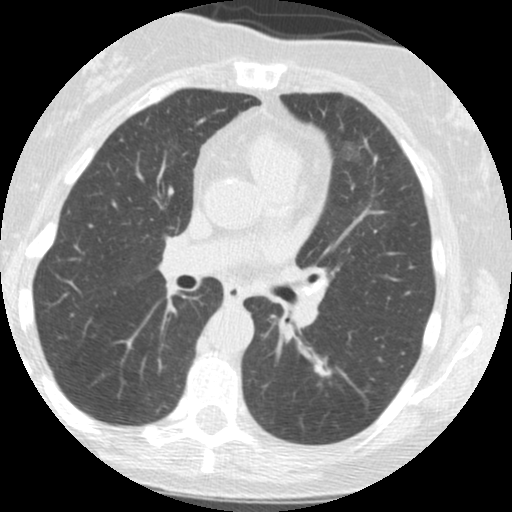
Chest CT (low-dose screening protocol), one axial image, first (baseline) screen, lung window (W 1500 / L -600 HU), 2.5 mm slice thickness, standard (soft-tissue) reconstruction kernel (STANDARD), slice 66 of 147 in the series, 512 × 512 image matrix. Female participant, aged 61 years at enrolment. Current smoker at enrolment.
Expert-annotated lung lesion, bounding box <303,342,351,392> (left, top, right, bottom; pixels). Screening reader's record for this exam (one nodule recorded; not confirmed to be the boxed lesion): non-calcified nodule or mass ≥4 mm, left lower lobe, 12 × 11 mm, spiculated (stellate) margins, soft tissue attenuation. Official screen result: positive, change unspecified: nodule(s) >= 4 mm or enlarging nodule(s), mass(es), or other non-specific abnormalities suspicious for lung cancer. Later outcome: lung cancer diagnosed 440 days after this screen — squamous cell carcinoma, NOS, left lower lobe, moderately differentiated (G2), stage IA (AJCC 6th edition), 12 mm at pathology.